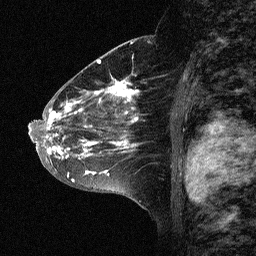
Breast MRI (dynamic contrast-enhanced), one sagittal slice; position 36 of 64 along the scan axis; dynamic contrast-enhanced study with each time point stored as its own series, time point 2 of 3 at this slice position (early post-contrast, ordered by acquisition time); 1.5 T; TE 4.5 ms, TR 11 ms; 256 × 256 image matrix, field of view 200 × 200 mm. Female patient, age 46 years. From the clinical record (not read from this slice): setting: breast cancer imaged before/during neoadjuvant chemotherapy; receptor status: HER2-positive.
Annotated regions visible in this slice (semi-automatically segmented with operator editing):
- analysis volume of interest (the breast-tissue region the enhancement analysis was run in; not a lesion): bounding box [x1, y1, x2, y2] px = [43, 72, 165, 177]
- tumour enhancement mask (voxels above the 90 % enhancement threshold inside the analysis volume of interest): [44, 74, 141, 174]